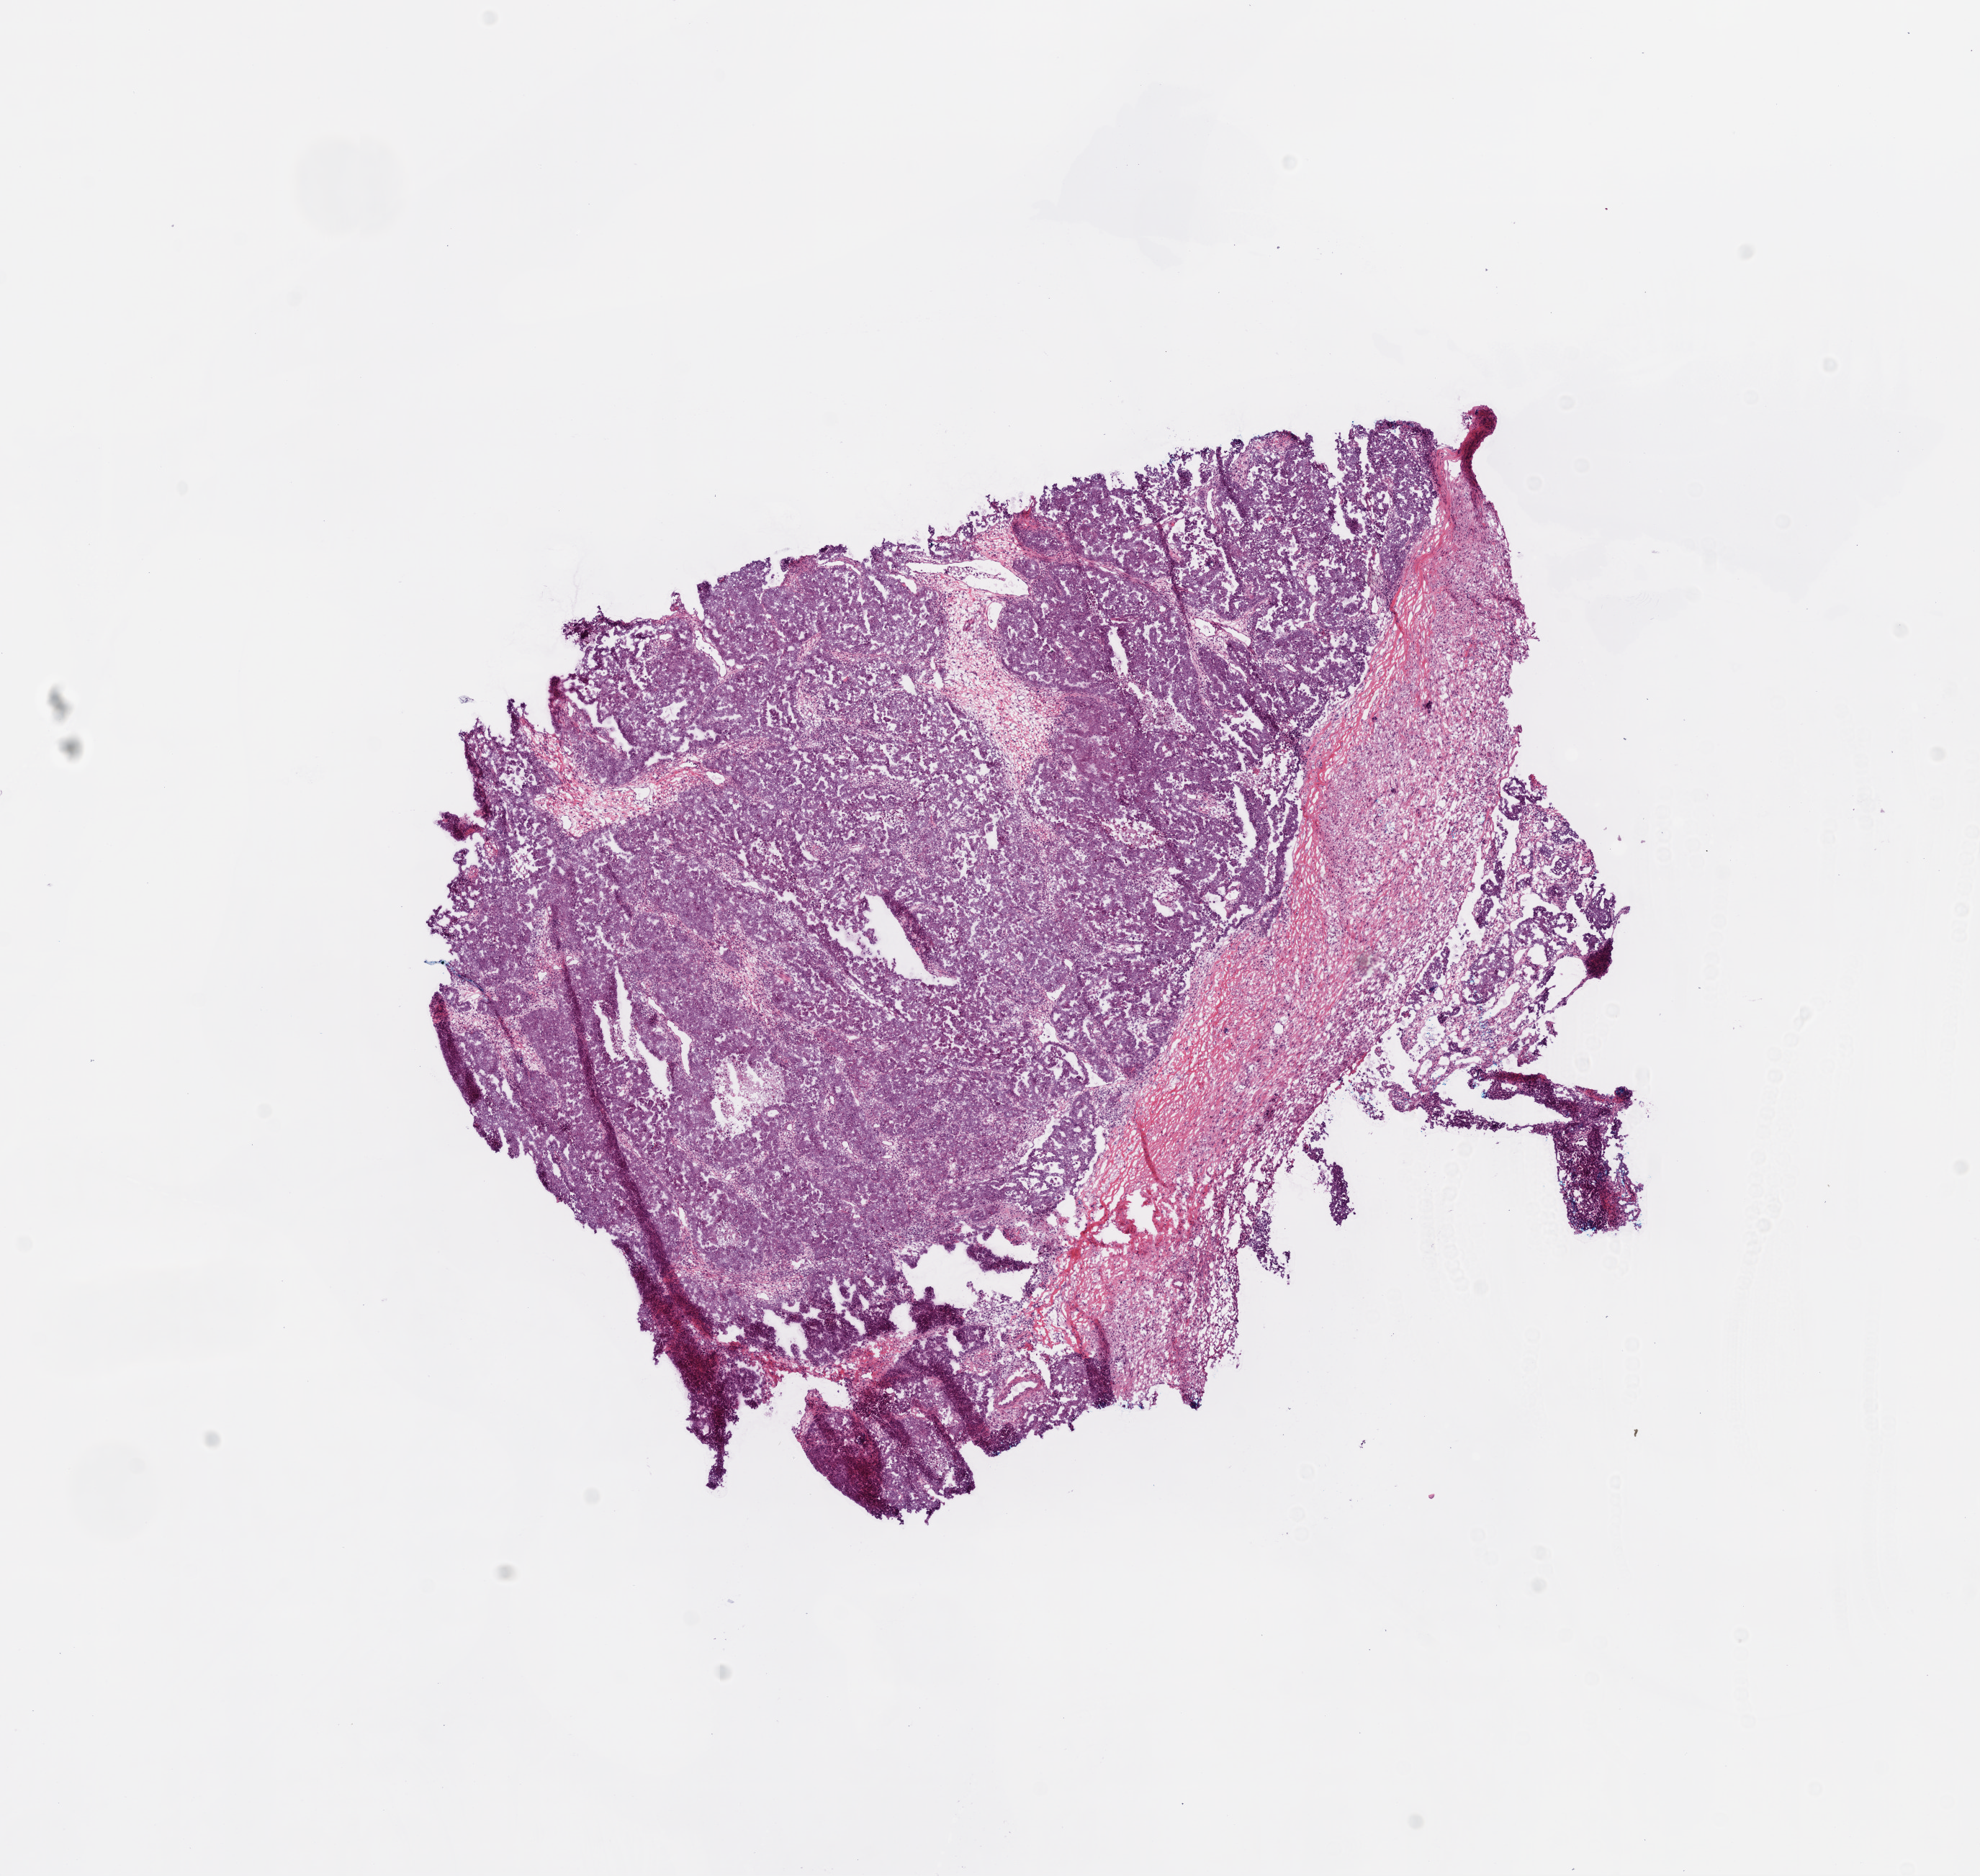
Whole-slide histology image, H&E-stained — a low-resolution overview of the entire scanned area, about 11.0 x 10.5 mm (from a 20x scan); frozen section from the top of the tissue portion; sample: primary tumour, ovary. Patient: female, age at initial diagnosis 54 years. Histologic grade: G3 (poorly differentiated). Pathologist review of this section (percent, as recorded): tumour cells 80%, tumour nuclei 90%, normal cells 0%, stromal cells 20%, necrosis 0%.
- laterality: right
- pathologic diagnosis: Serous cystadenocarcinoma, NOS
- FIGO stage: IIIC